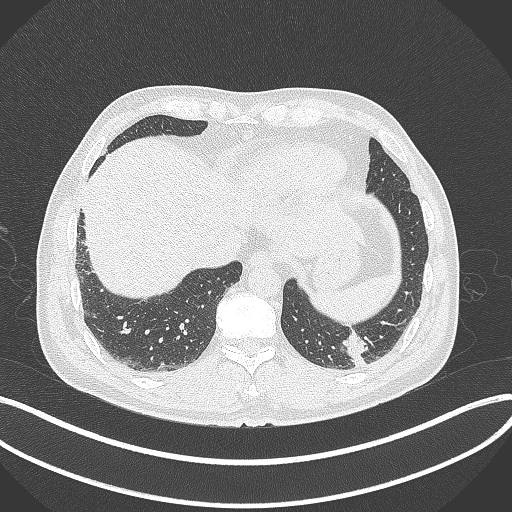
Chest CT, one axial slice; position 56 of 300 along the scan axis; 120 kVp; lung window (W 1500 / L -600 HU); 1 mm slice thickness; 512 × 512 image matrix. Patient: male, 54 years. Case-level facts recorded for this patient, not image findings: clinical TNM (as recorded): T1c N0 M1; histopathological grade: G3.
Outlined on this slice (bounding box drawn by a radiologist):
- lung tumour (recorded histology: adenocarcinoma): bounding box (x1, y1, x2, y2) in pixels: (343, 328, 369, 359)